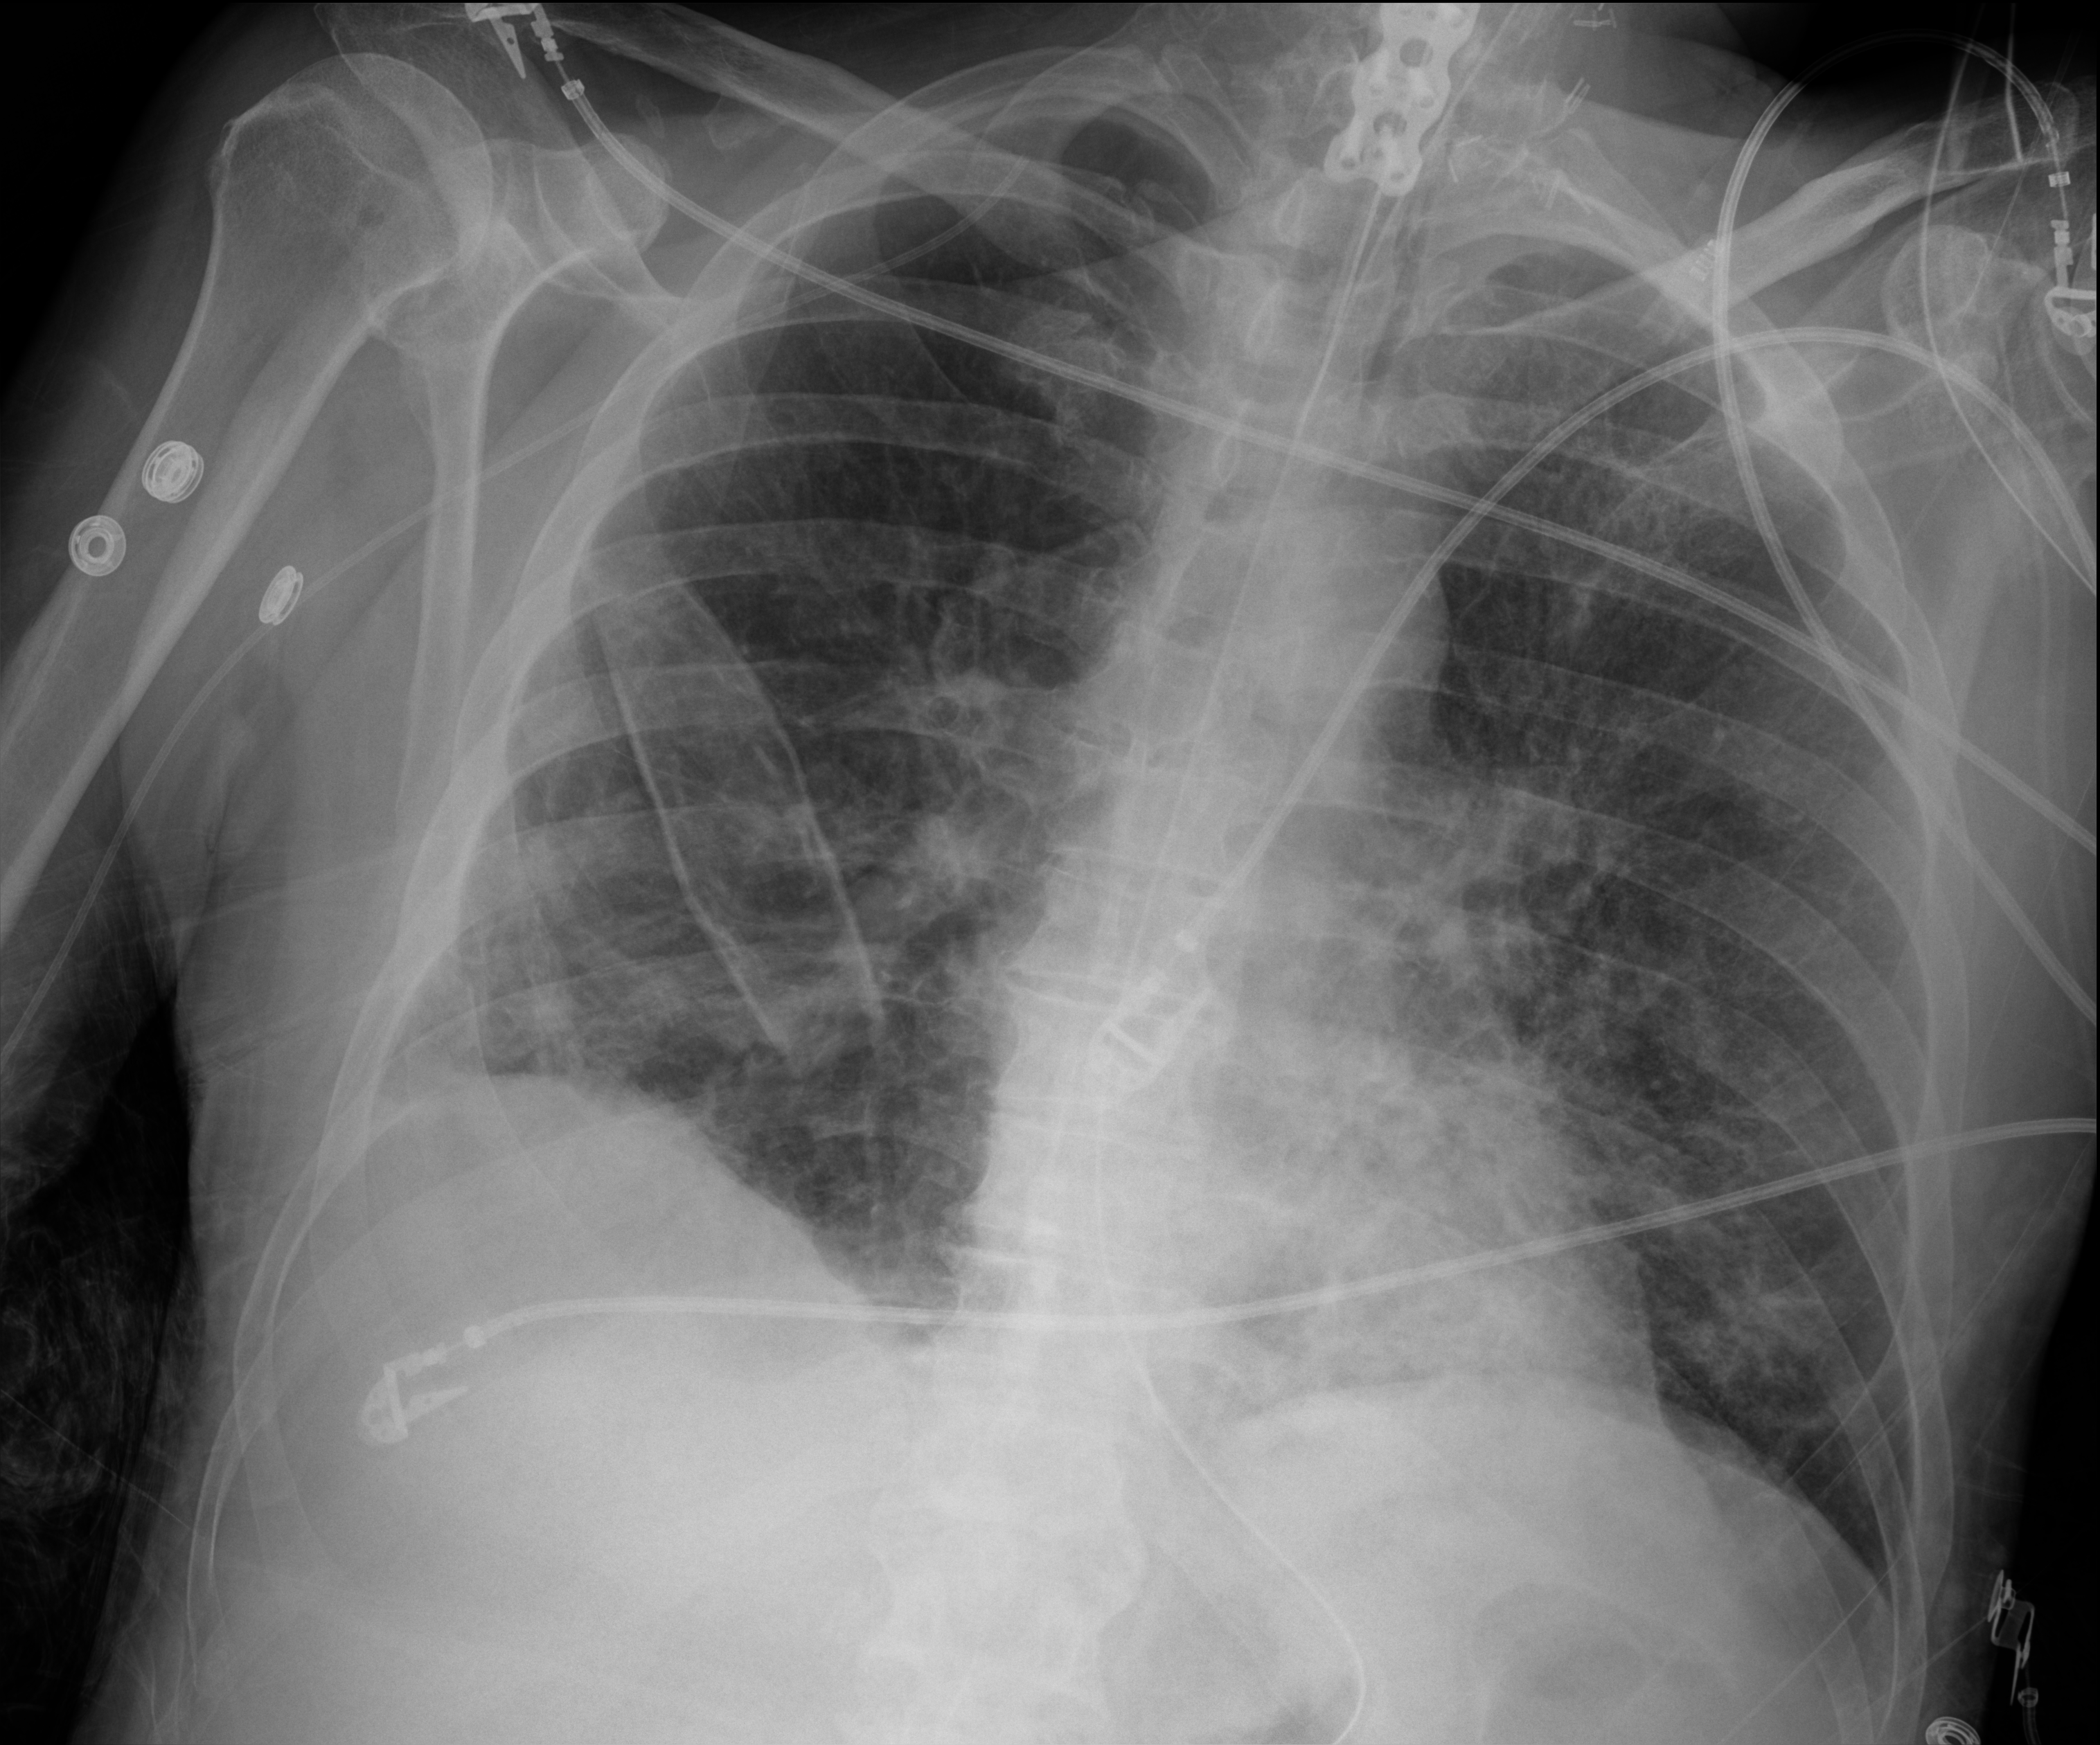
Chest X-ray (portable); anteroposterior (AP) projection. Male patient hospitalised with COVID-19, age 60–74 years.
Admission-level facts for this patient (not findings on this image; timing relative to this image not recorded): mechanically ventilated during this hospital stay: yes; length of hospital stay: 43 days.